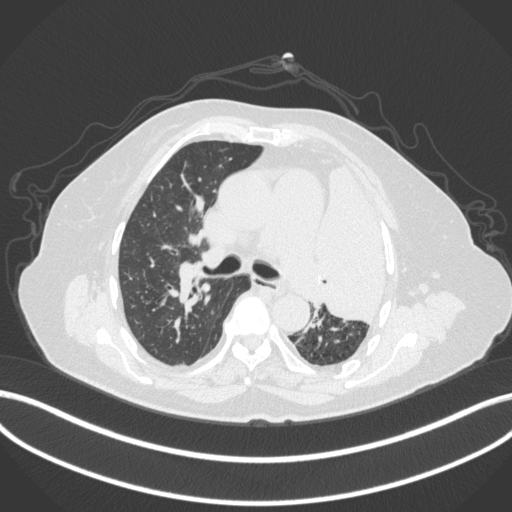
Chest CT, one axial slice; position 245 of 399 along the scan axis; 120 kVp; lung window (W 1500 / L -600 HU); 1 mm slice thickness; 512 × 512 image matrix. Female patient, age 75 years. Case-level facts recorded for this patient, not image findings: clinical TNM (as recorded): T3 N3 M1.
Annotated regions visible in this slice (rectangle marked by the reading radiologist):
- lung tumour (recorded histology: adenocarcinoma): bounding box [x1, y1, x2, y2] px = [308, 158, 390, 328]